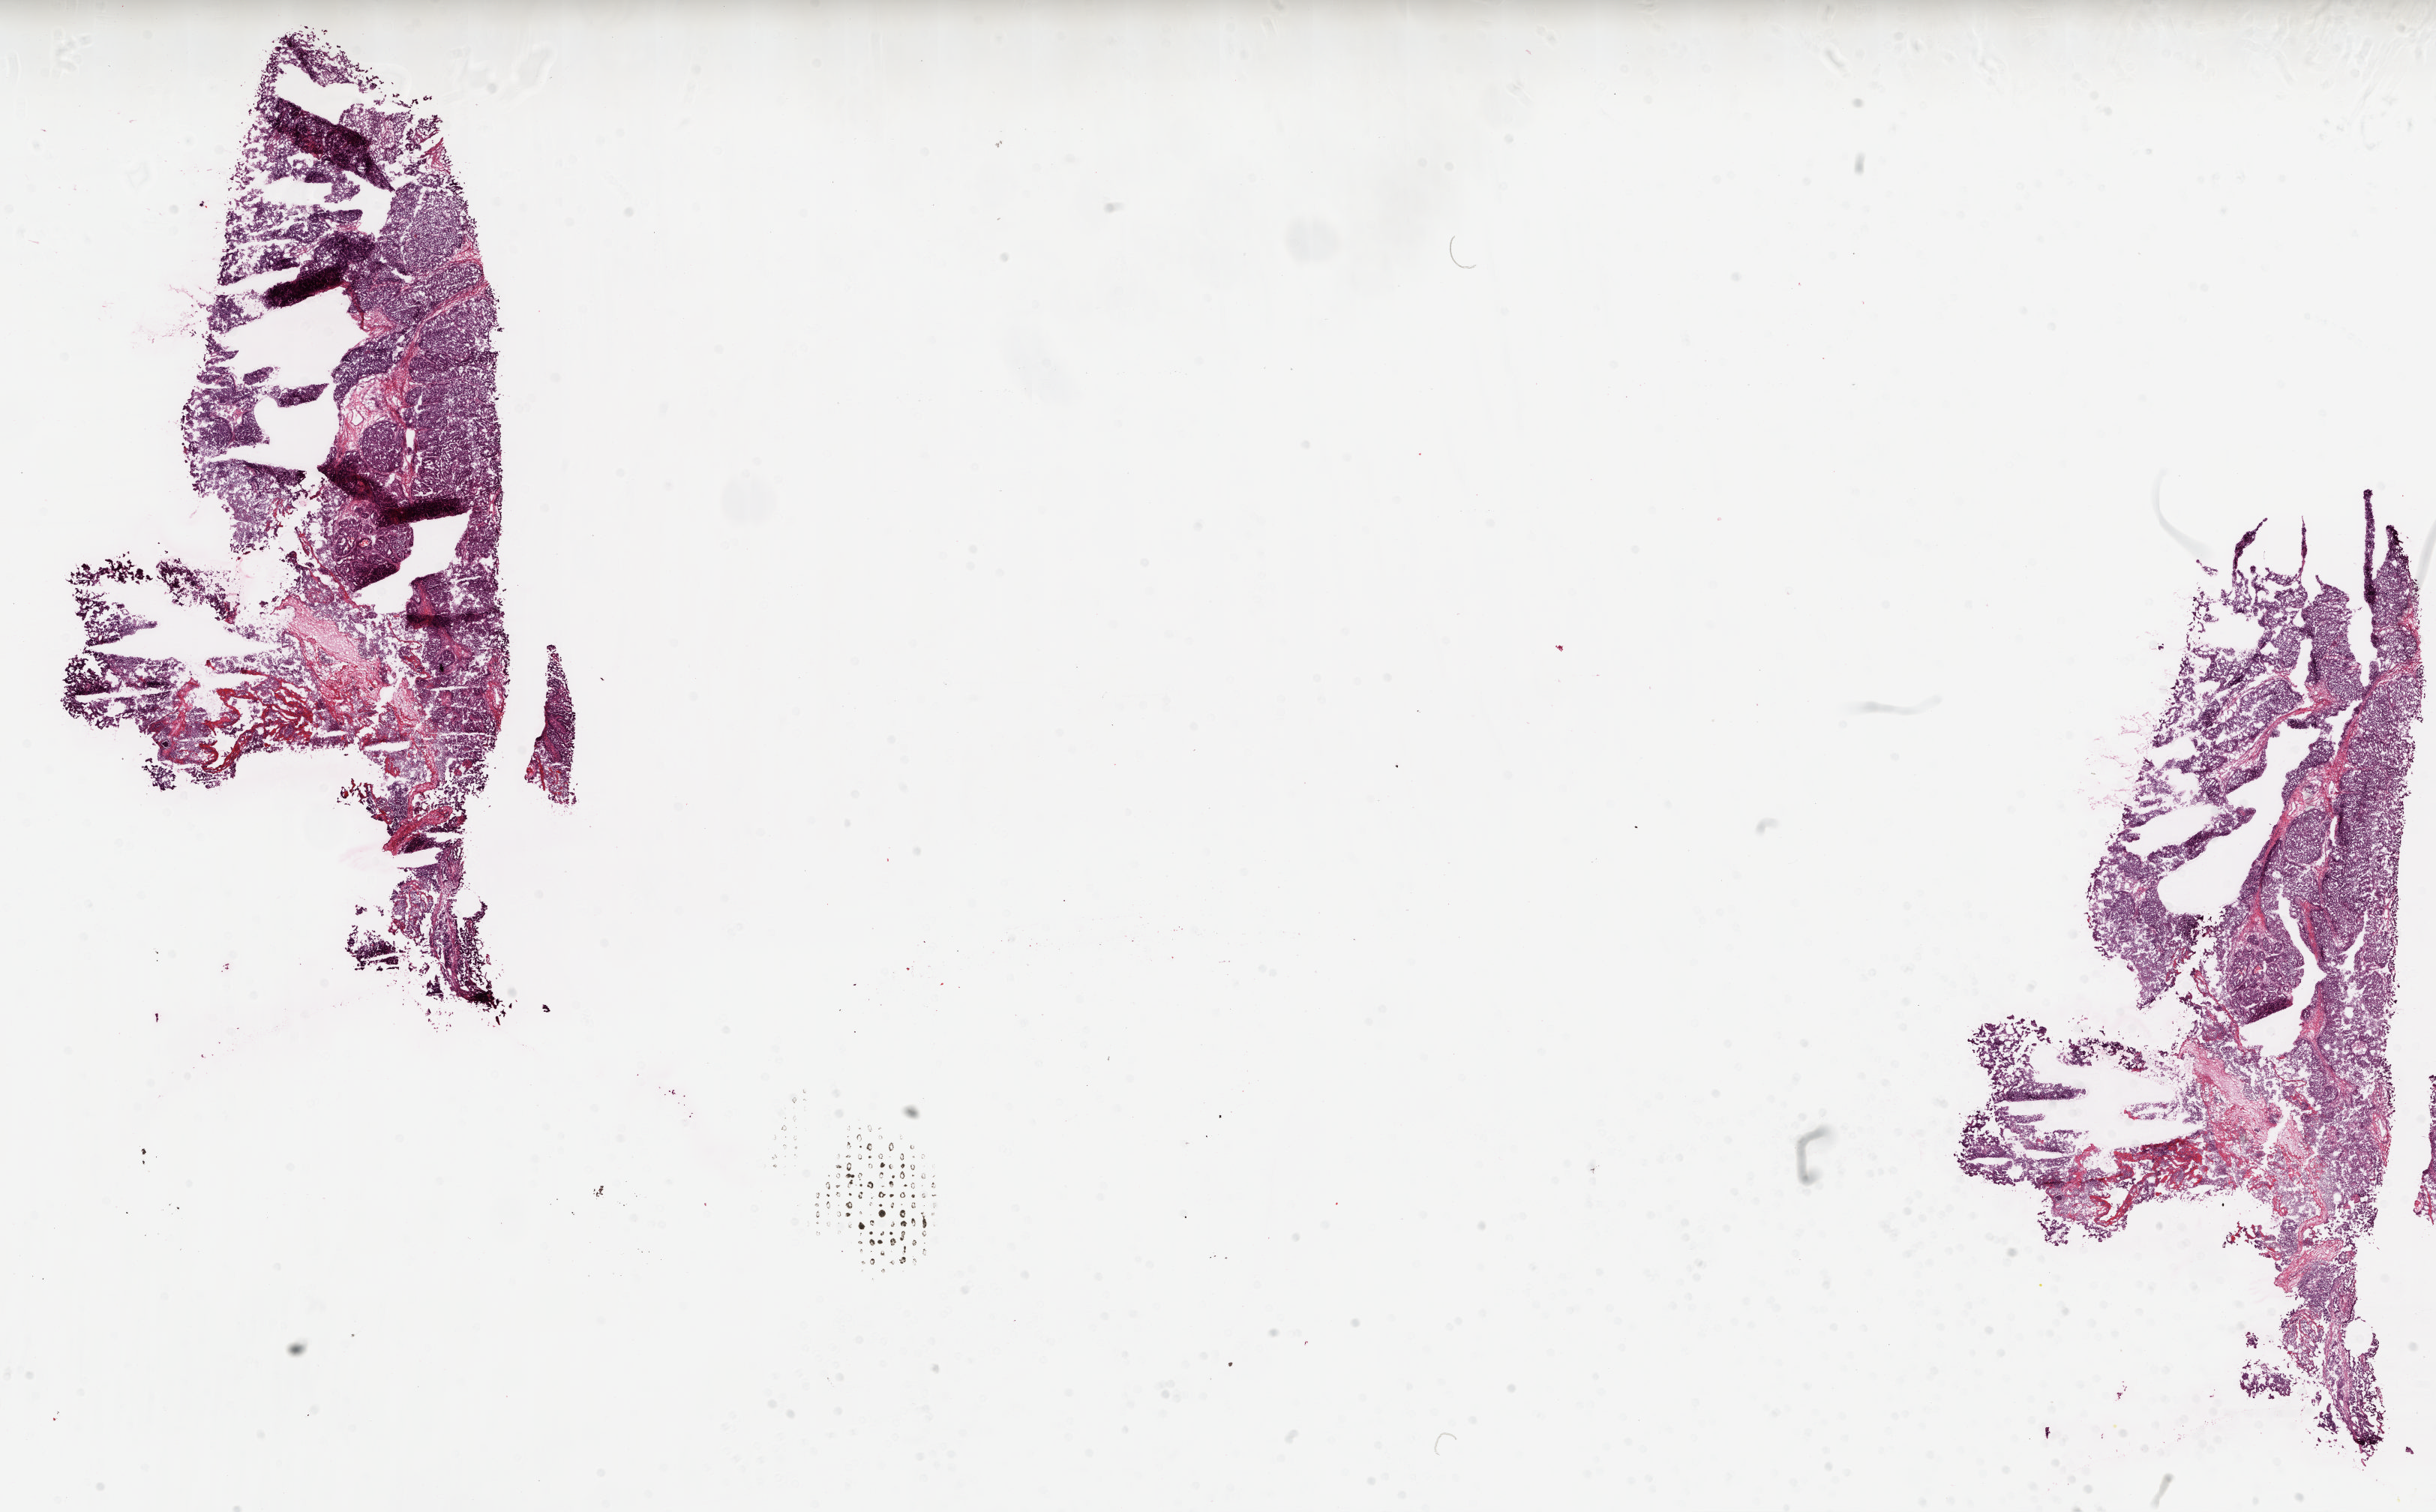
Digitized Hematoxylin and eosin (H&E) stained tissue section (whole slide), shown as a low-resolution overview of the whole scanned area (about 25.8 x 16.0 mm), frozen section from the top of the tissue portion, sample: primary tumour, ovary. Female, age 48 years at initial diagnosis. Histologic grade: G3 (poorly differentiated). Slide review estimates, as recorded: tumour cells 85%, tumour nuclei 95%, normal cells 0%, stromal cells 15%, necrosis 0%.
Laterality: left. FIGO stage: IA. Diagnosis: Serous cystadenocarcinoma, NOS.